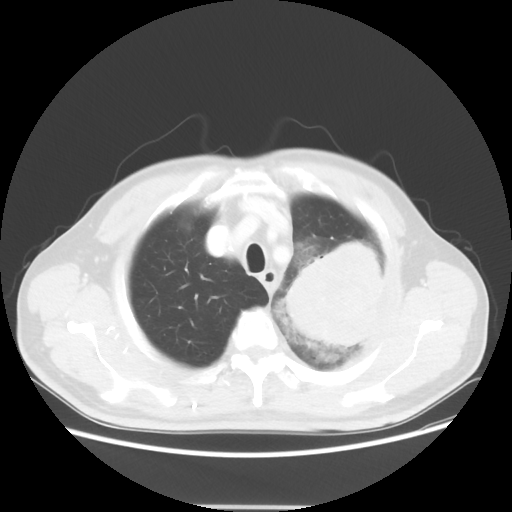
Chest CT, one axial slice. Position 46 of 53 along the scan axis. 100 kVp. Lung window (W 1500 / L -600 HU). 512 × 512 image matrix, field of view 391 × 391 mm. Male patient, age 60 years. Case-level facts recorded for this patient, not image findings: clinical TNM (as recorded): T4 N1 M1a; histopathological grade: G3.
Structures marked on this image (rectangle marked by the reading radiologist):
- lung tumour (recorded histology: large cell carcinoma): bounding box (x1, y1, x2, y2) in pixels: (264, 239, 386, 346)